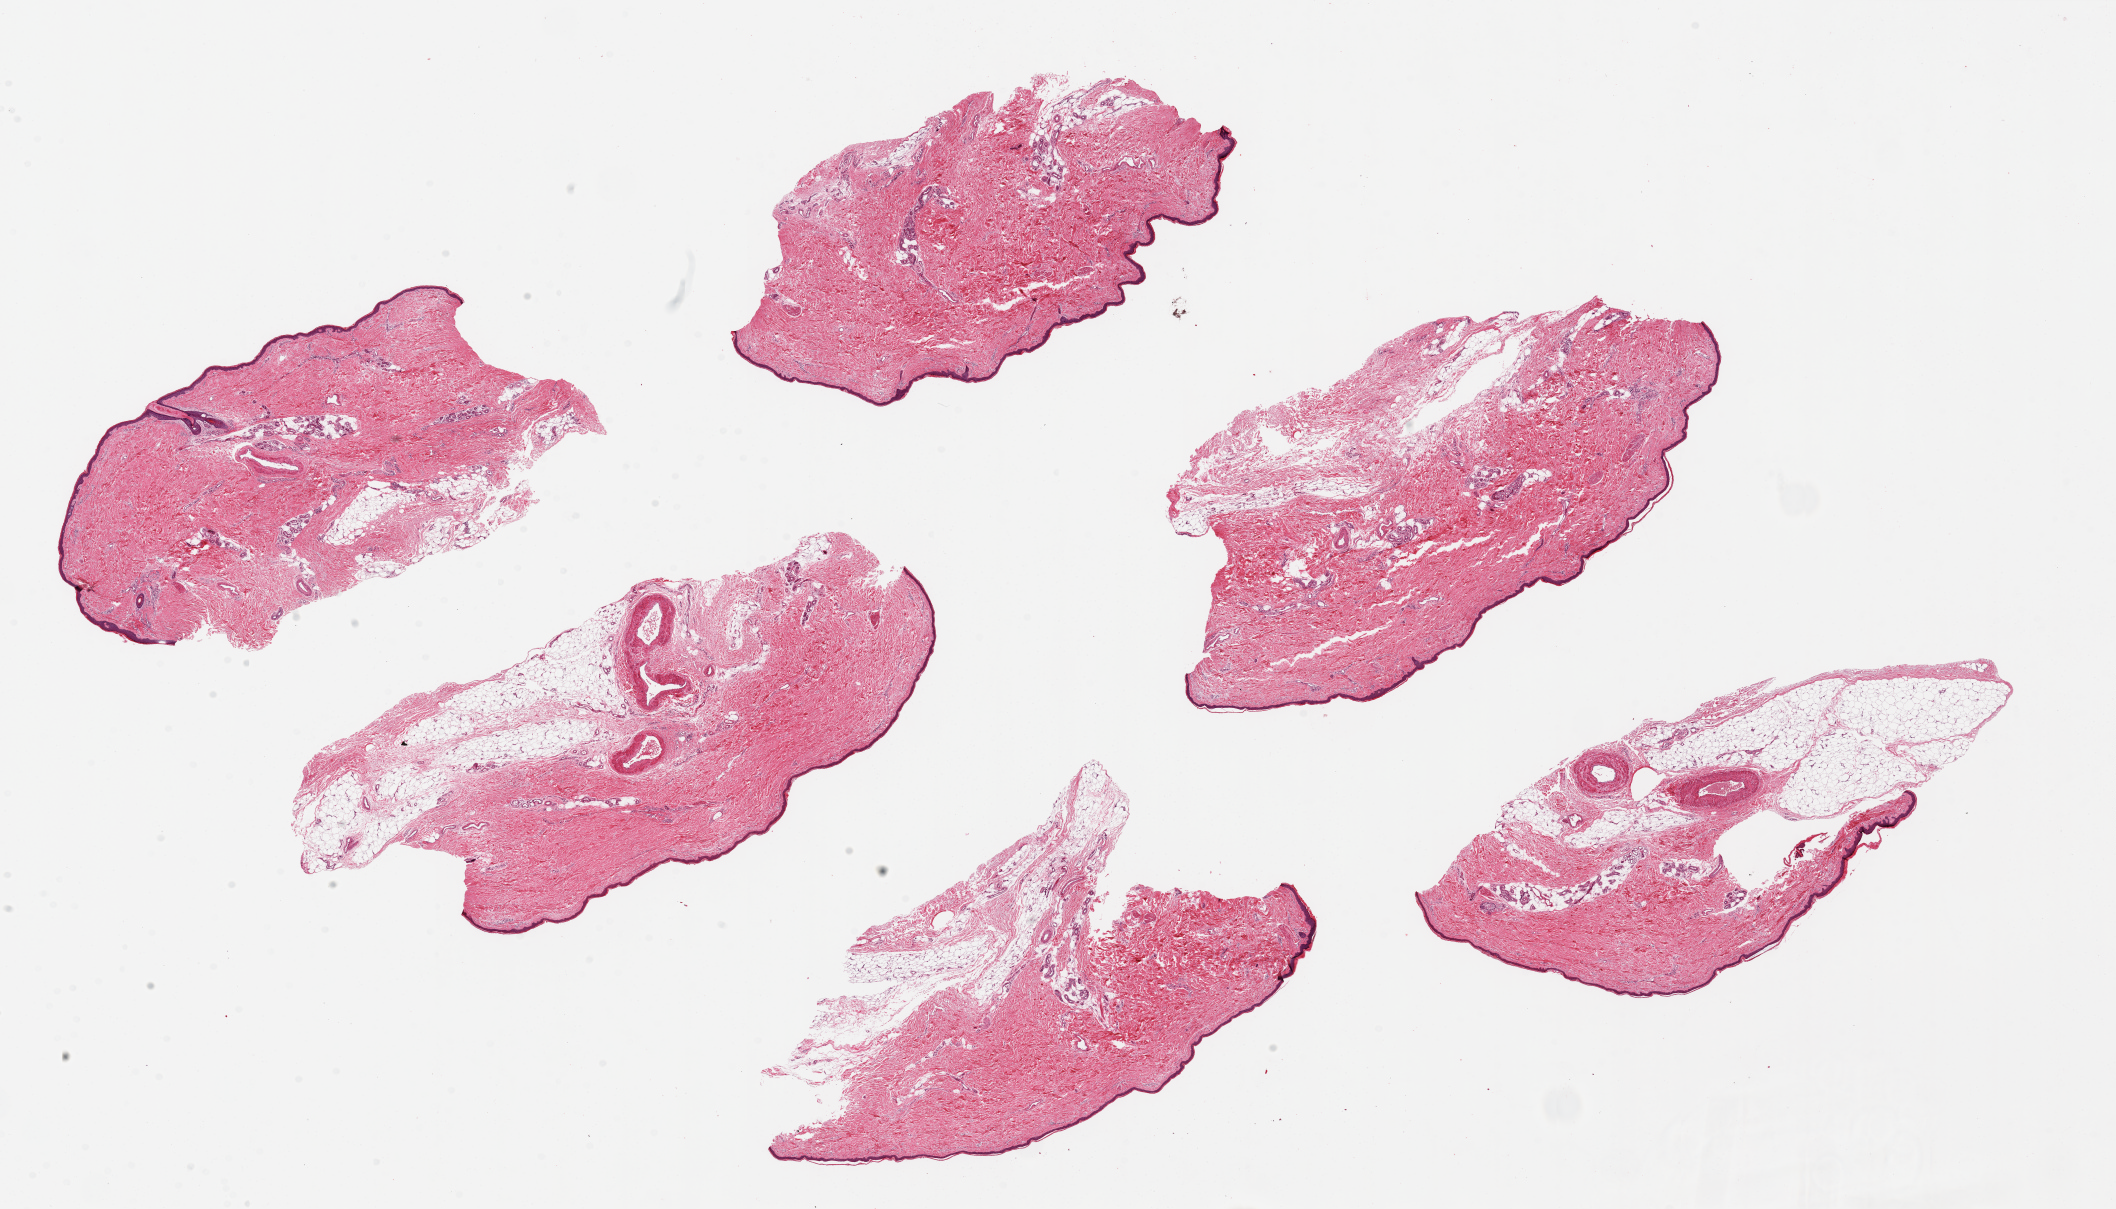
Haematoxylin and eosin whole-slide image, shown as a low-resolution overview of the whole scanned area (about 33.5 x 19.1 mm, from a 20x scan), PAXgene-fixed paraffin-embedded (PFPE) section, sampled site (target tissue): skin of lower leg, tissue donor sample.
- review note (as recorded): 6 pieces ~9x4mm. Squamous epithelium is ~1% of thickness